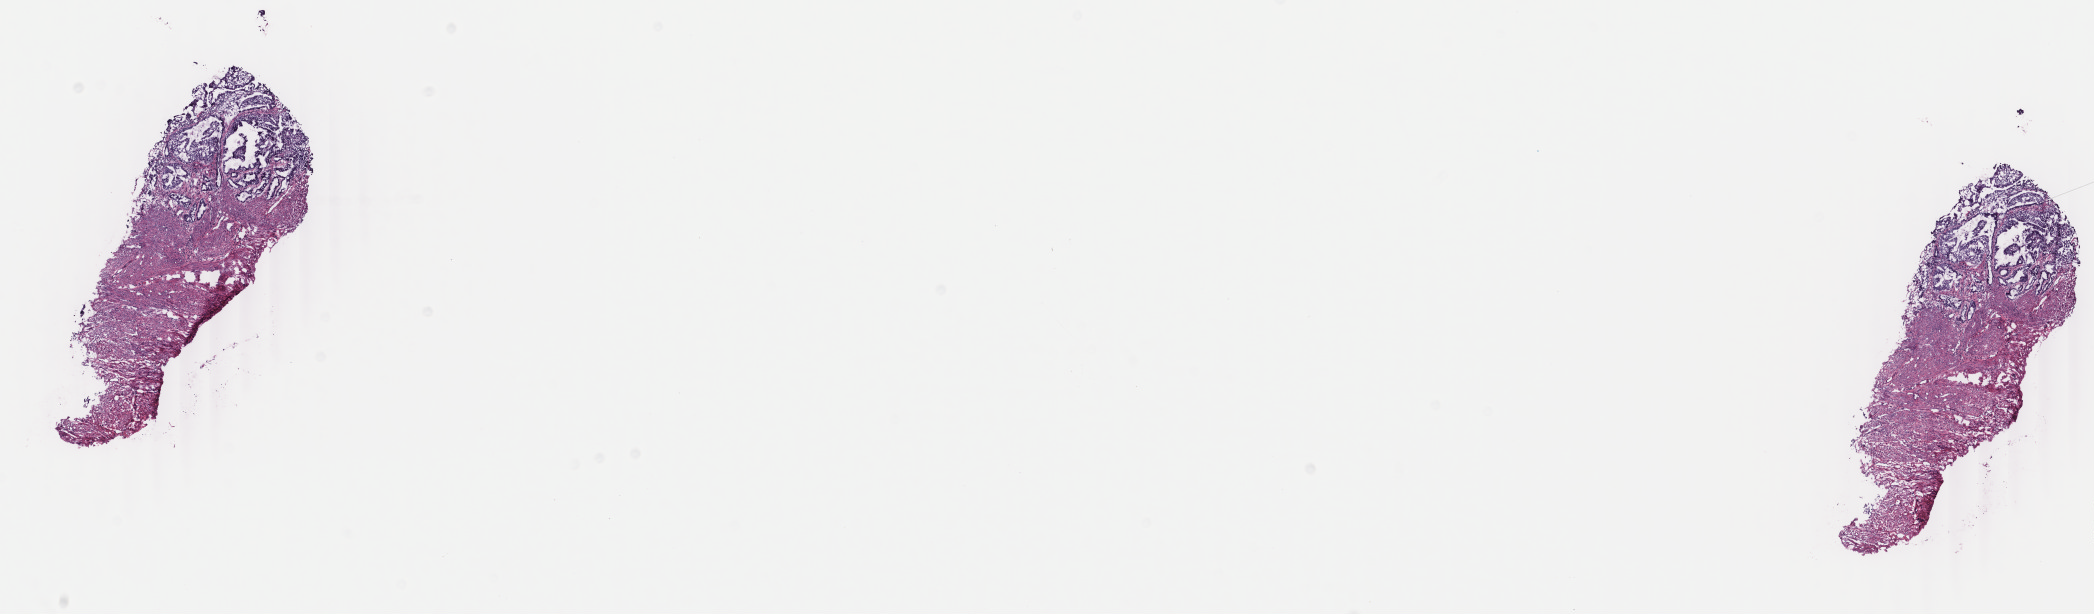
Whole-slide histology image, H&E — low-resolution overview of the scanned area, about 16.7 x 4.9 mm (slide scanned at 40x); frozen section from the bottom of the tissue portion; uterus, primary tumour sample. Female patient; age at initial diagnosis 75 years. Histologic grade: G1 (well differentiated). Pathologist review of this section (percent, as recorded): tumour cells 20%, tumour nuclei 30%, normal cells 70%, stromal cells 0%, necrosis 10%. Infiltration values recorded for this section: lymphocyte infiltration 20%, monocyte infiltration 0%, neutrophil infiltration 10%.
FIGO stage: IB. Histologic diagnosis: Endometrioid adenocarcinoma, NOS (endometrium).